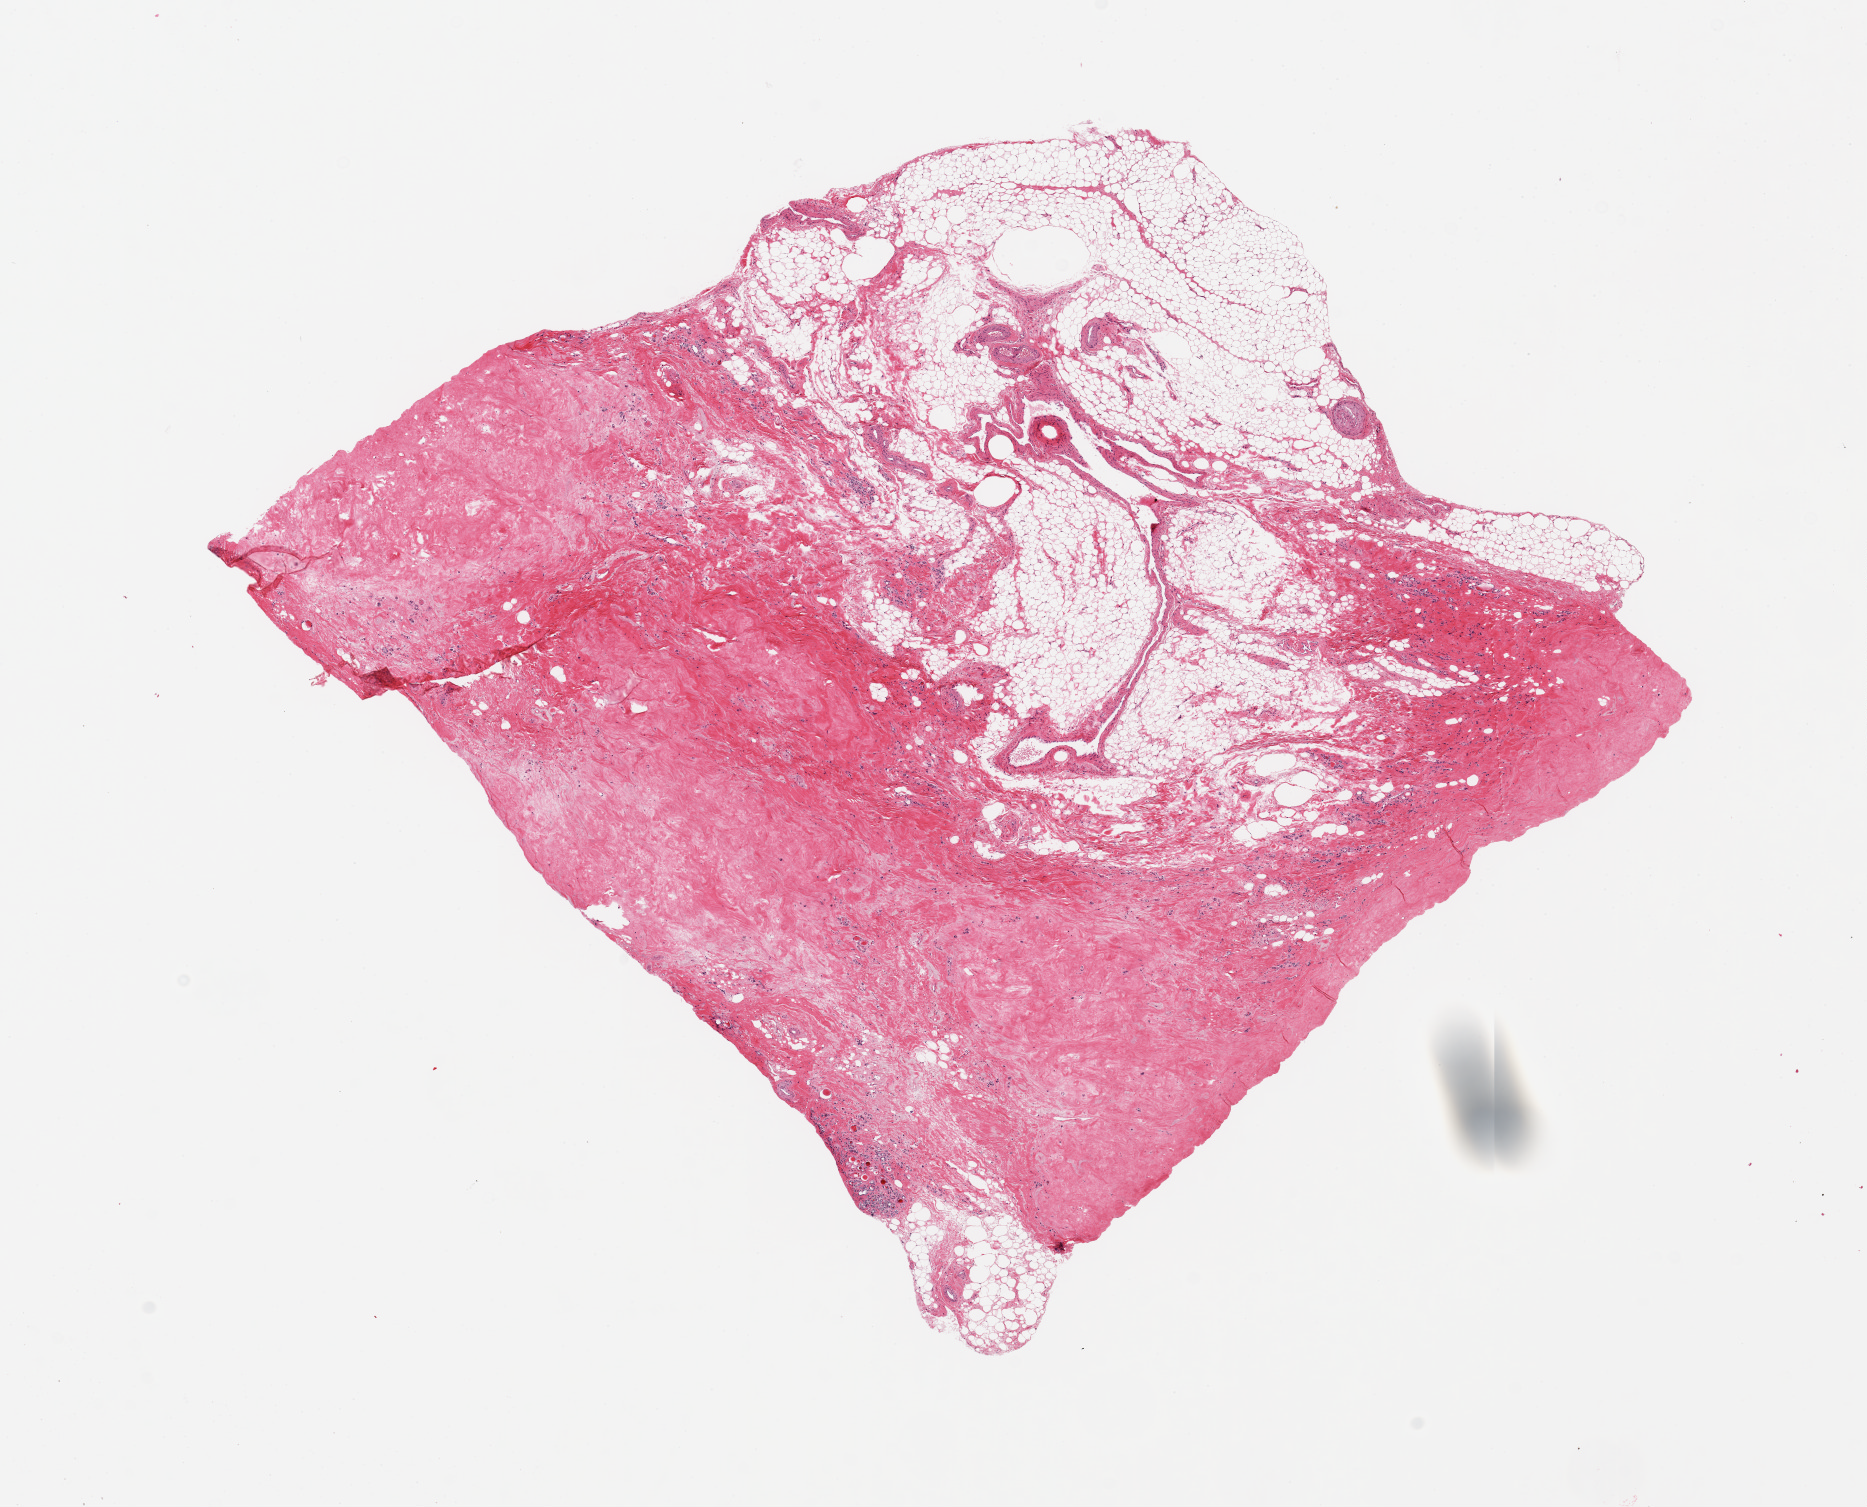
H&E whole-slide image, brightfield, a low-resolution overview of the entire scanned area, about 14.8 x 11.9 mm; PAXgene-fixed paraffin-embedded (PFPE) section; target tissue: thyroid; donor tissue sample. Female donor.
Reviewer comment on this tissue sample: 1 piece, 9x8mm; fibrofatty tissue with two very small fociof thyroid glands c/w irradiation.